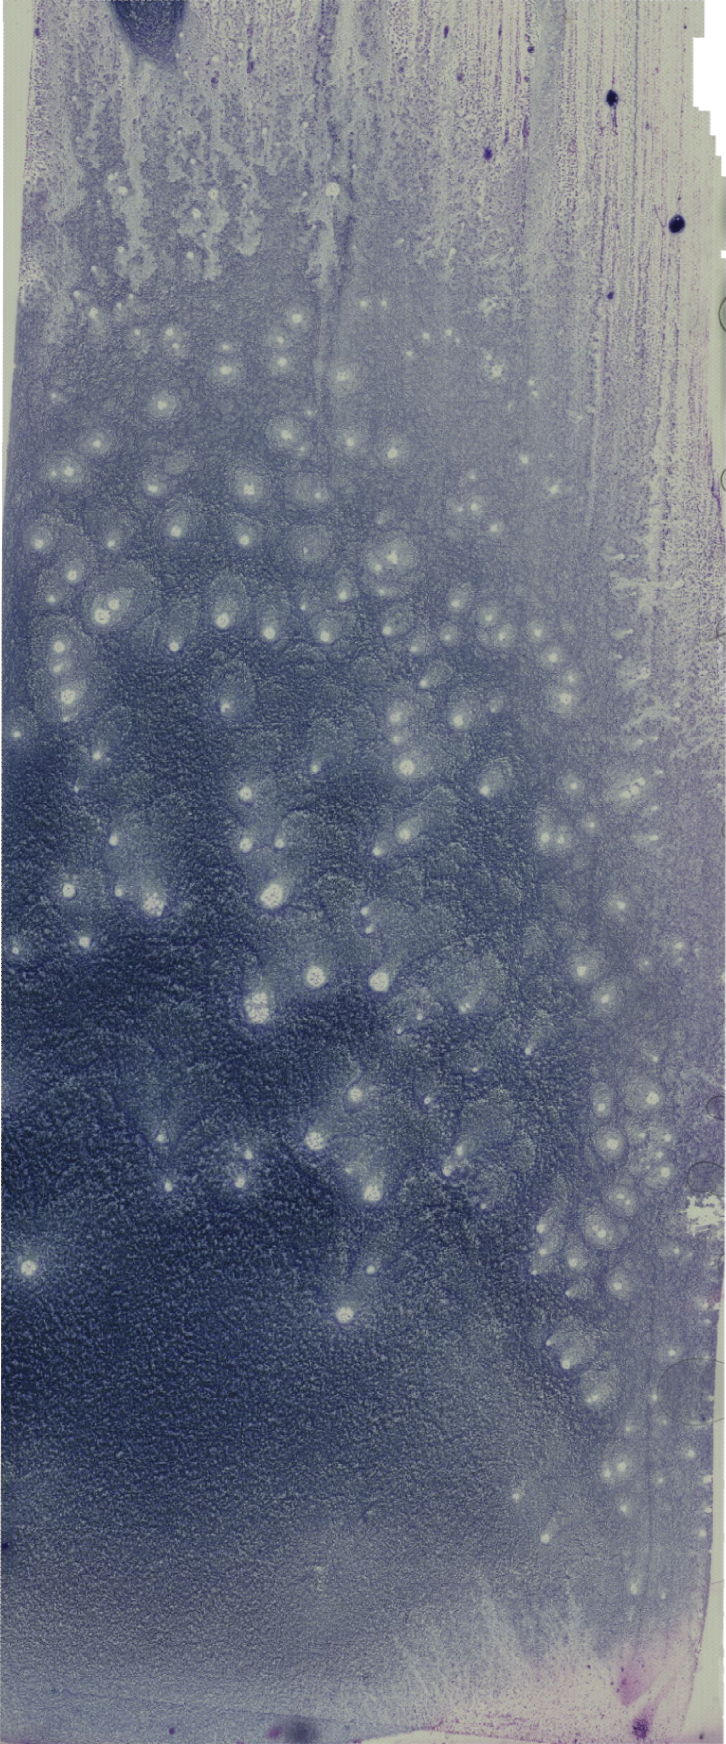
Bone marrow aspirate smear, May-Grünwald–Giemsa stain, whole-slide image, low-resolution overview of the scanned area, about 20.6 x 49.4 mm. Female patient.
* diagnosis: Mixed Phenotype Acute Leukemia, B/Myeloid